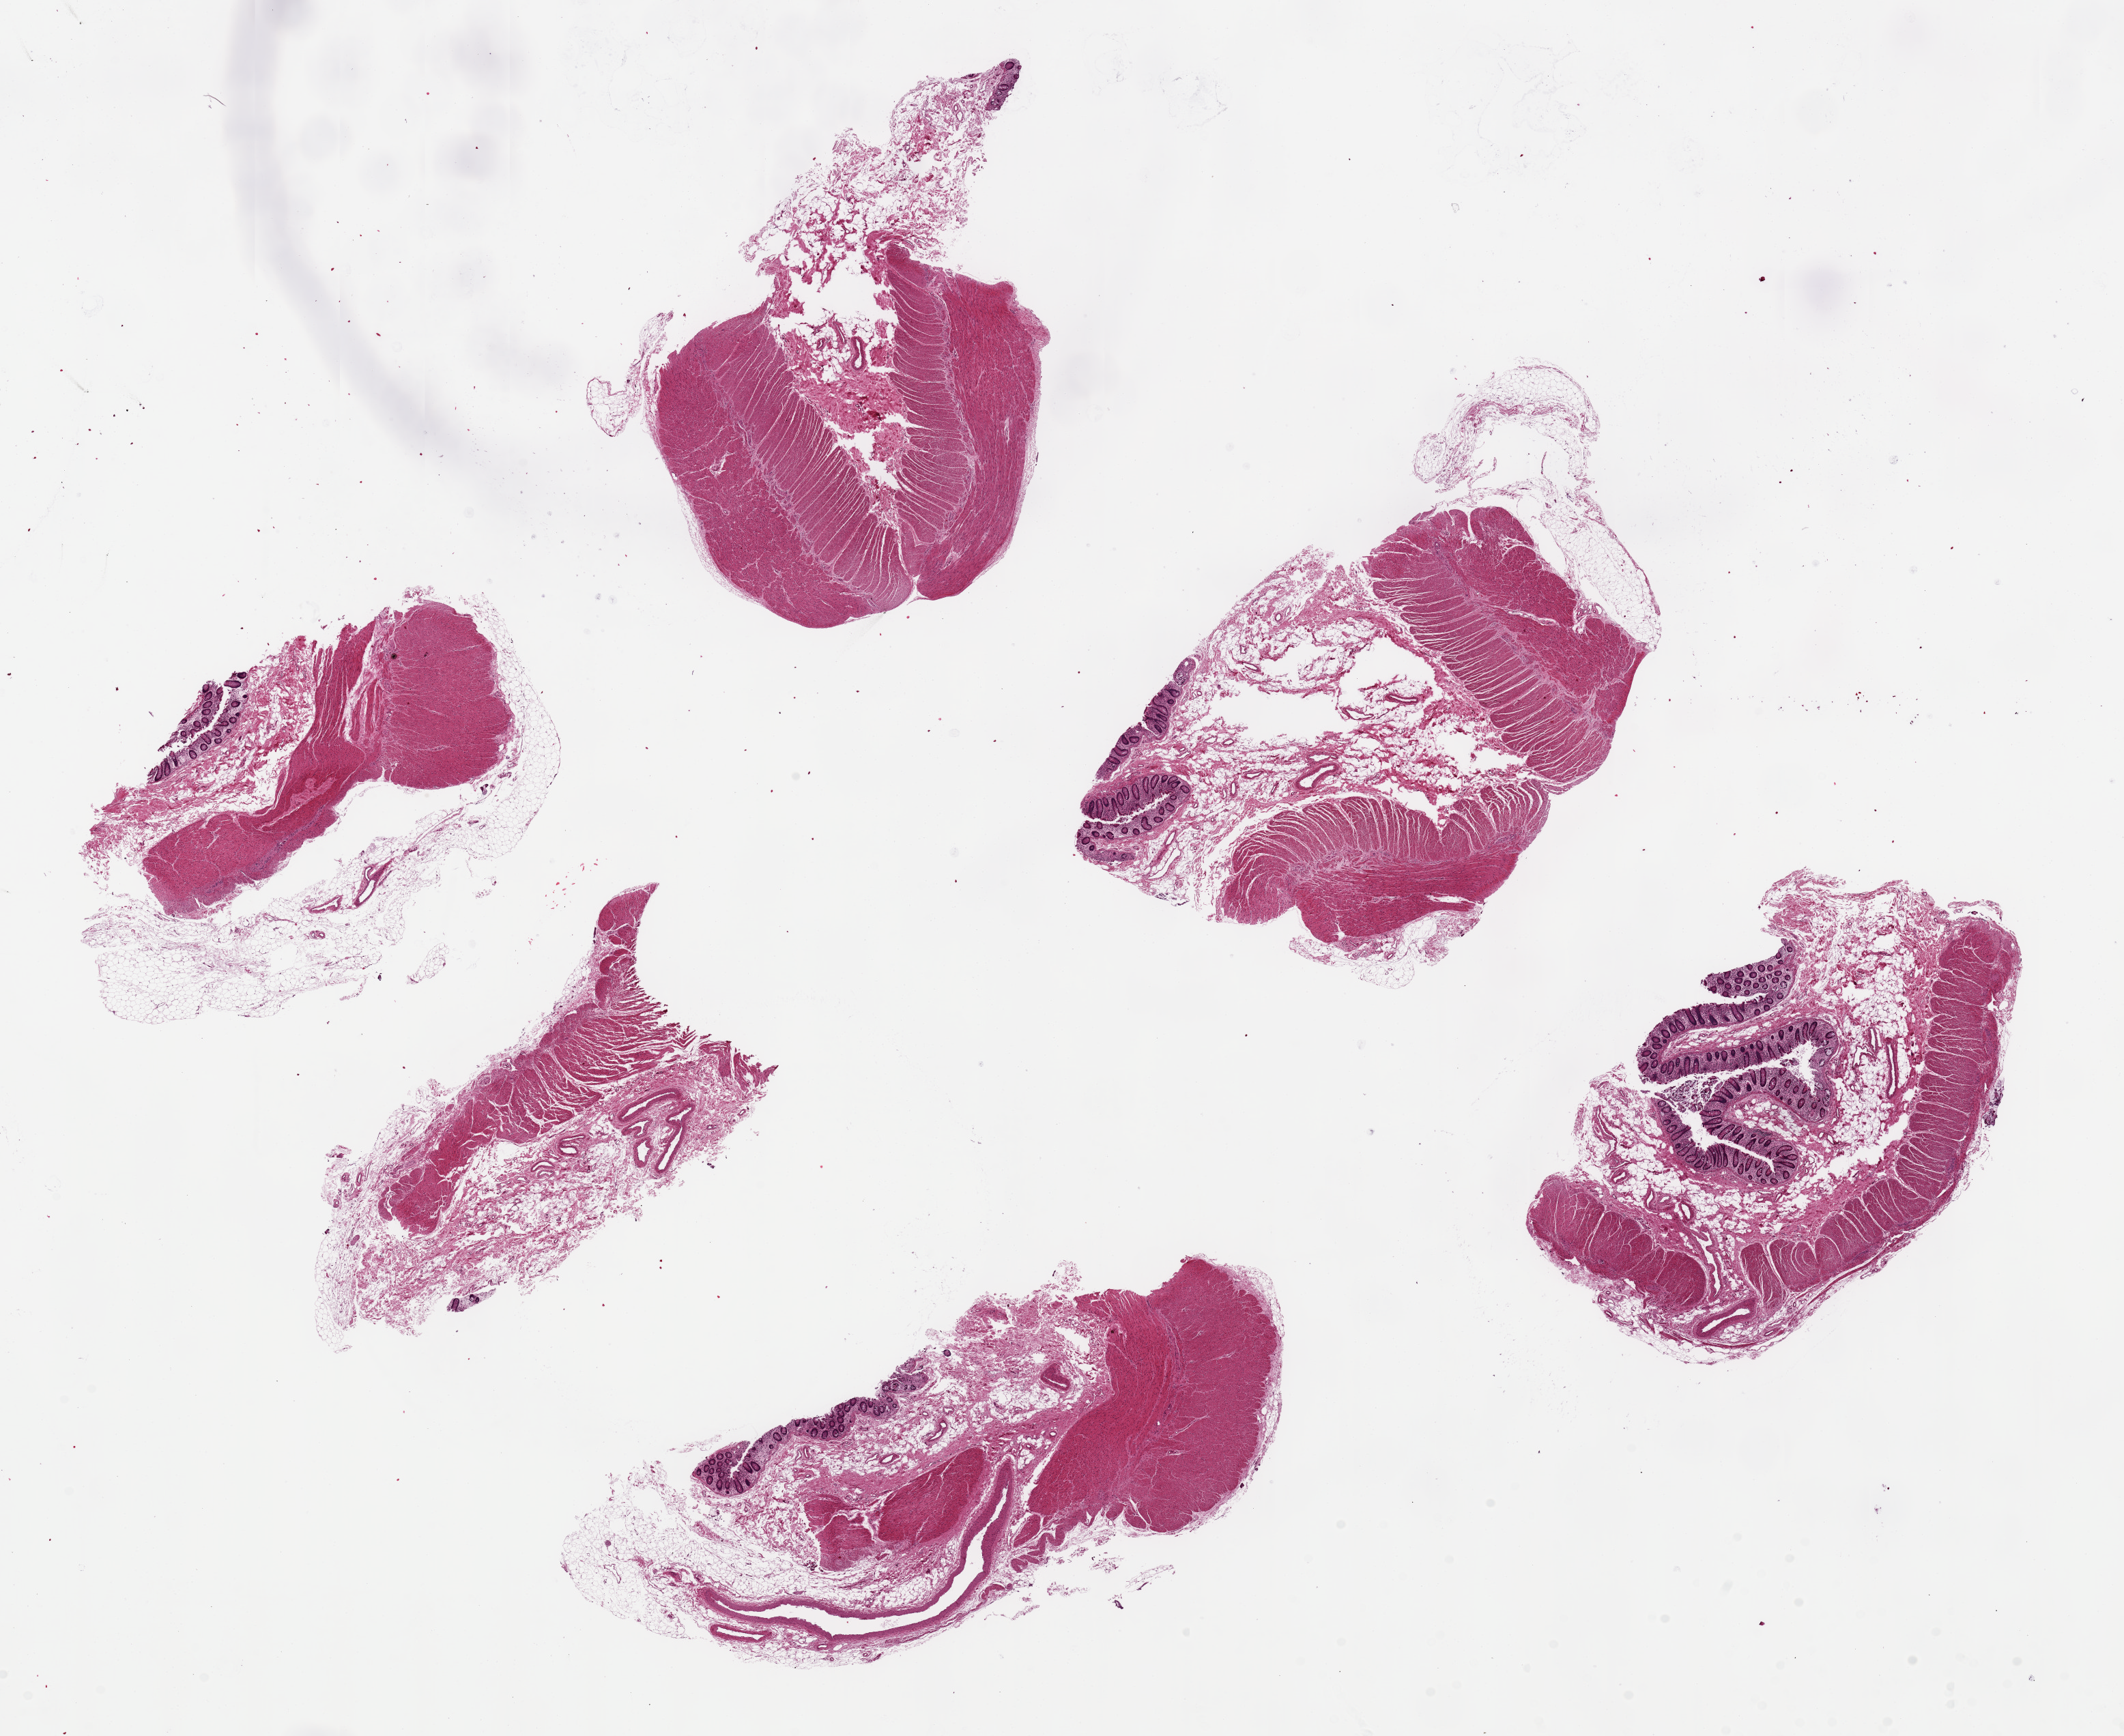
Hematoxylin and eosin (H&E) whole-slide image — low-resolution overview of the scanned area, about 24.6 x 20.1 mm. PAXgene-fixed, paraffin-embedded tissue. Sampled site (target tissue): transverse colon. Tissue donor sample.
- review note (as recorded): 6 pieces, ~6x3.5mm, poorly oriented with only minimal mucosa visible